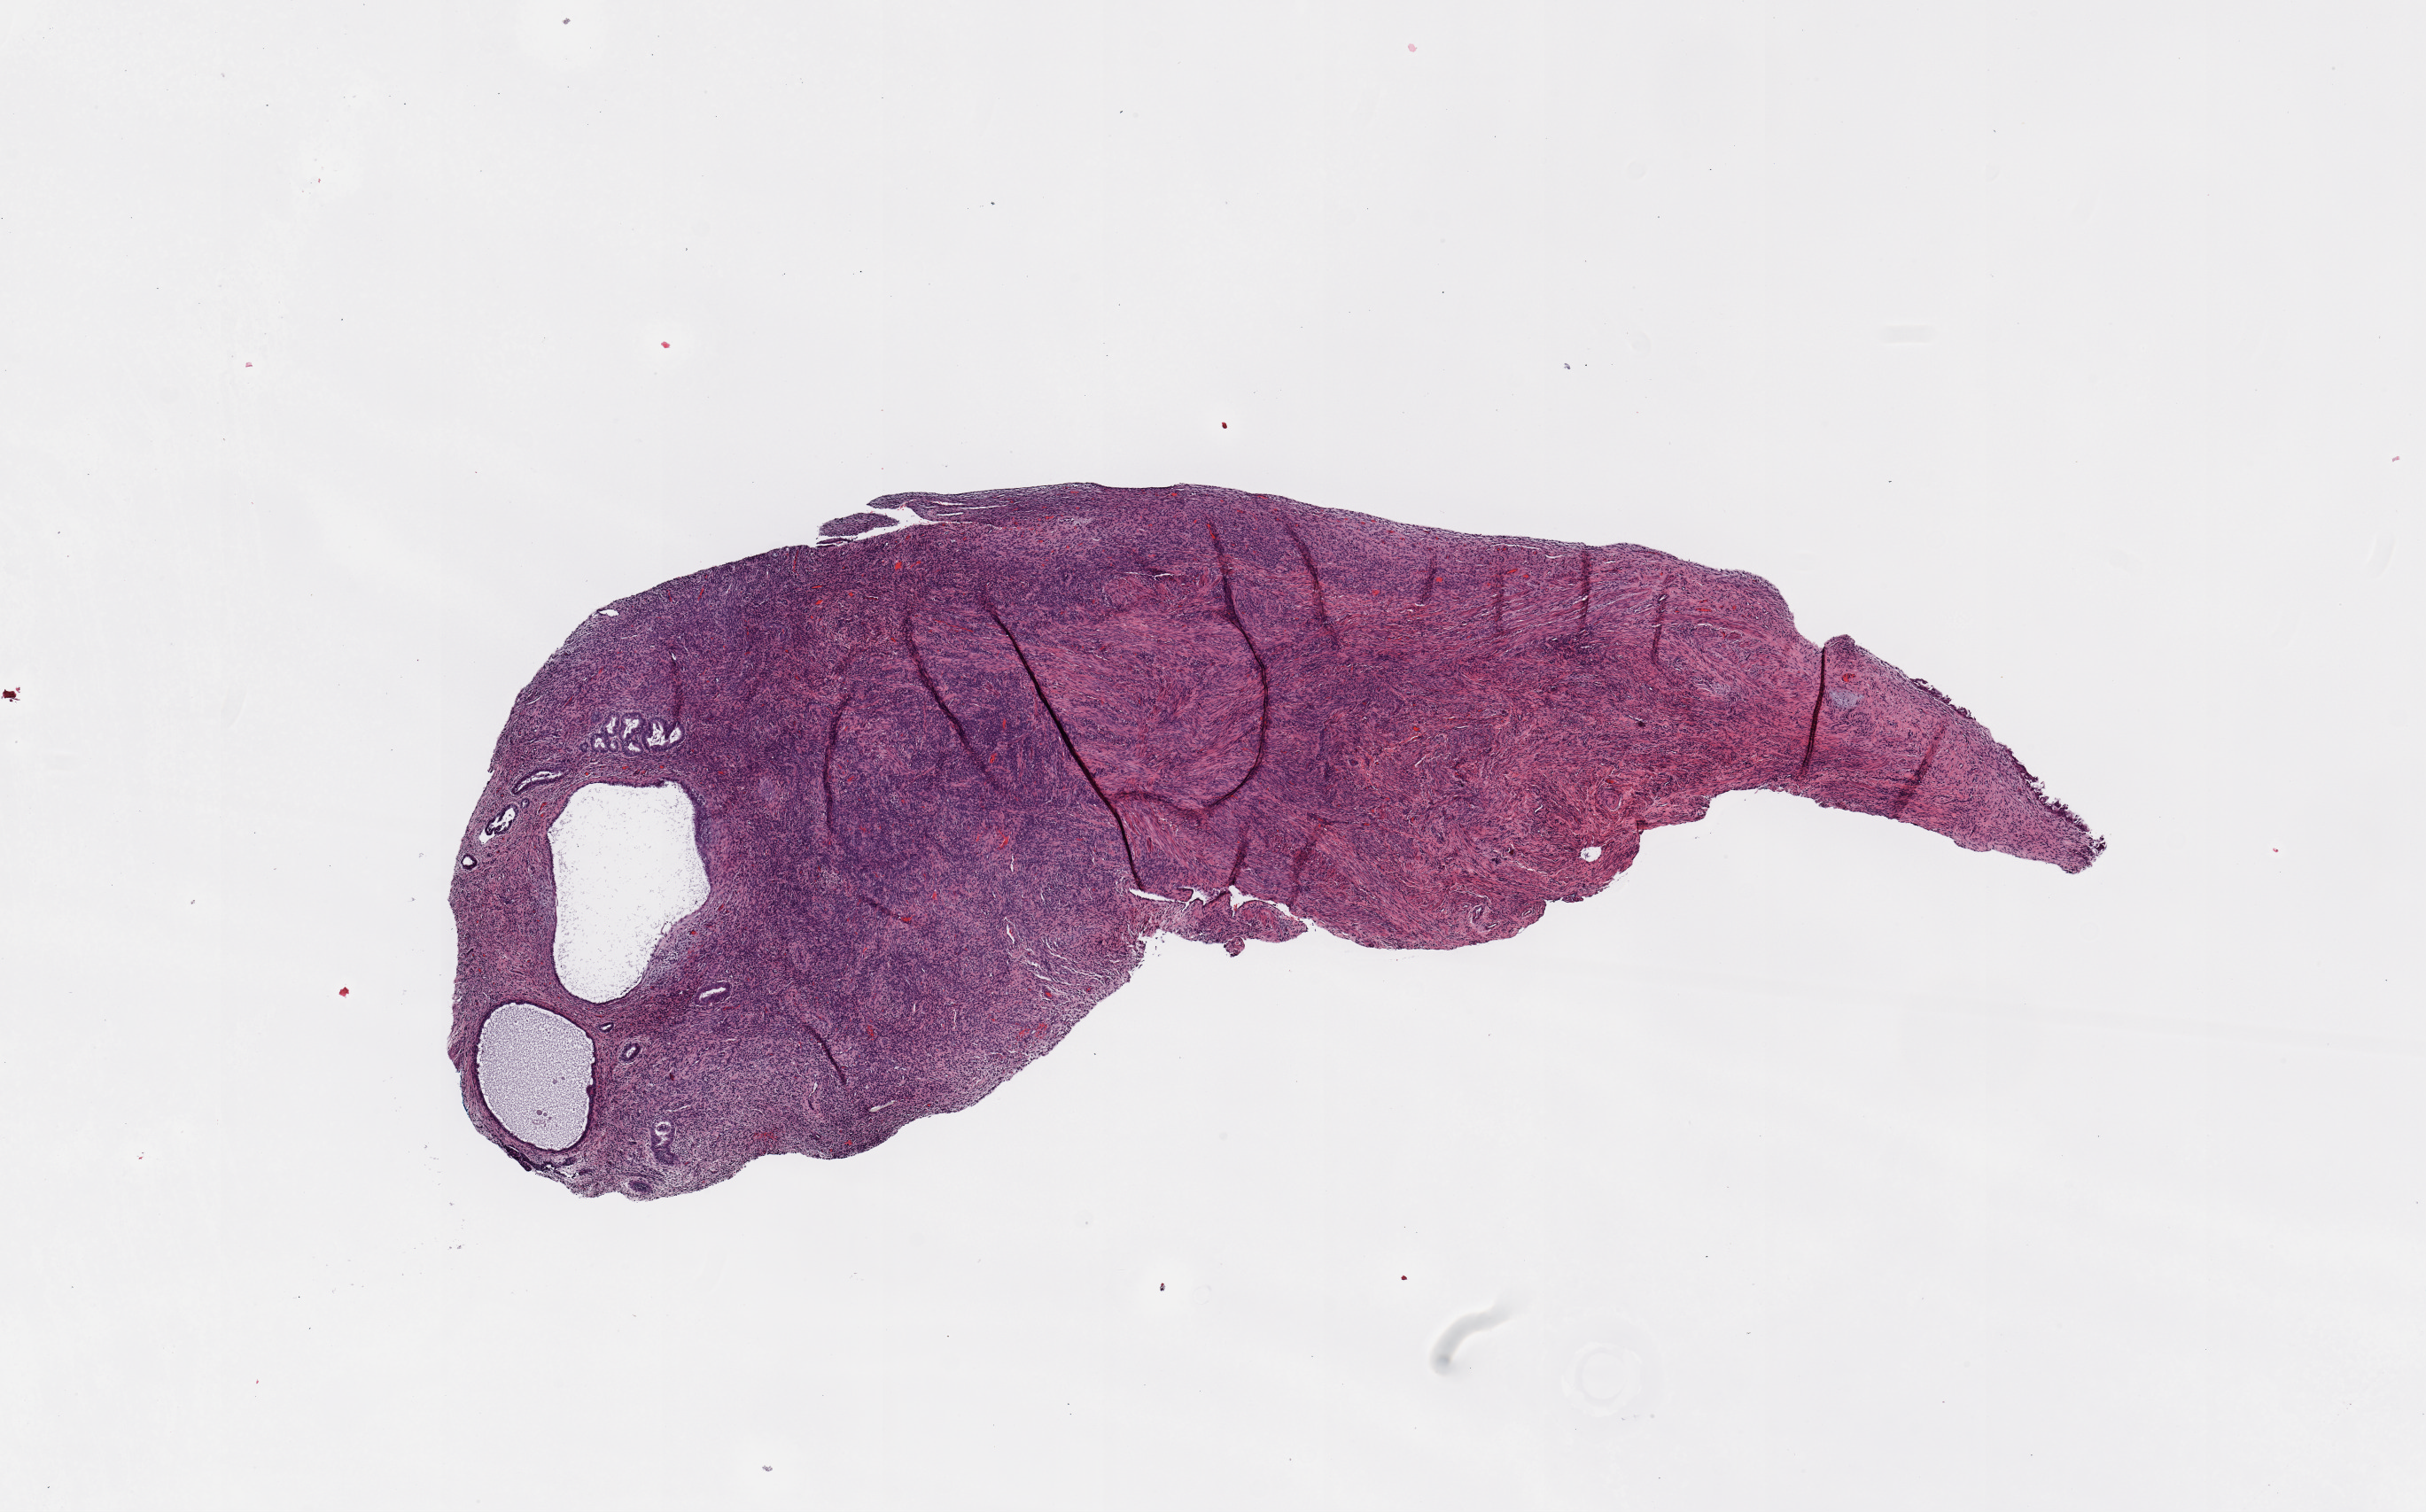
Digitized H&E-stained tissue section (whole slide) — whole scanned area (about 10.8 x 6.8 mm, acquisition: 20x scan) shown as a low-resolution overview. Normal (non-tumour) tissue sample, uterus. Patient: female, age 69 years.
• this section: normal (non-tumour) tissue from the same patient
• patient diagnosis: Endometrioid adenocarcinoma, NOS